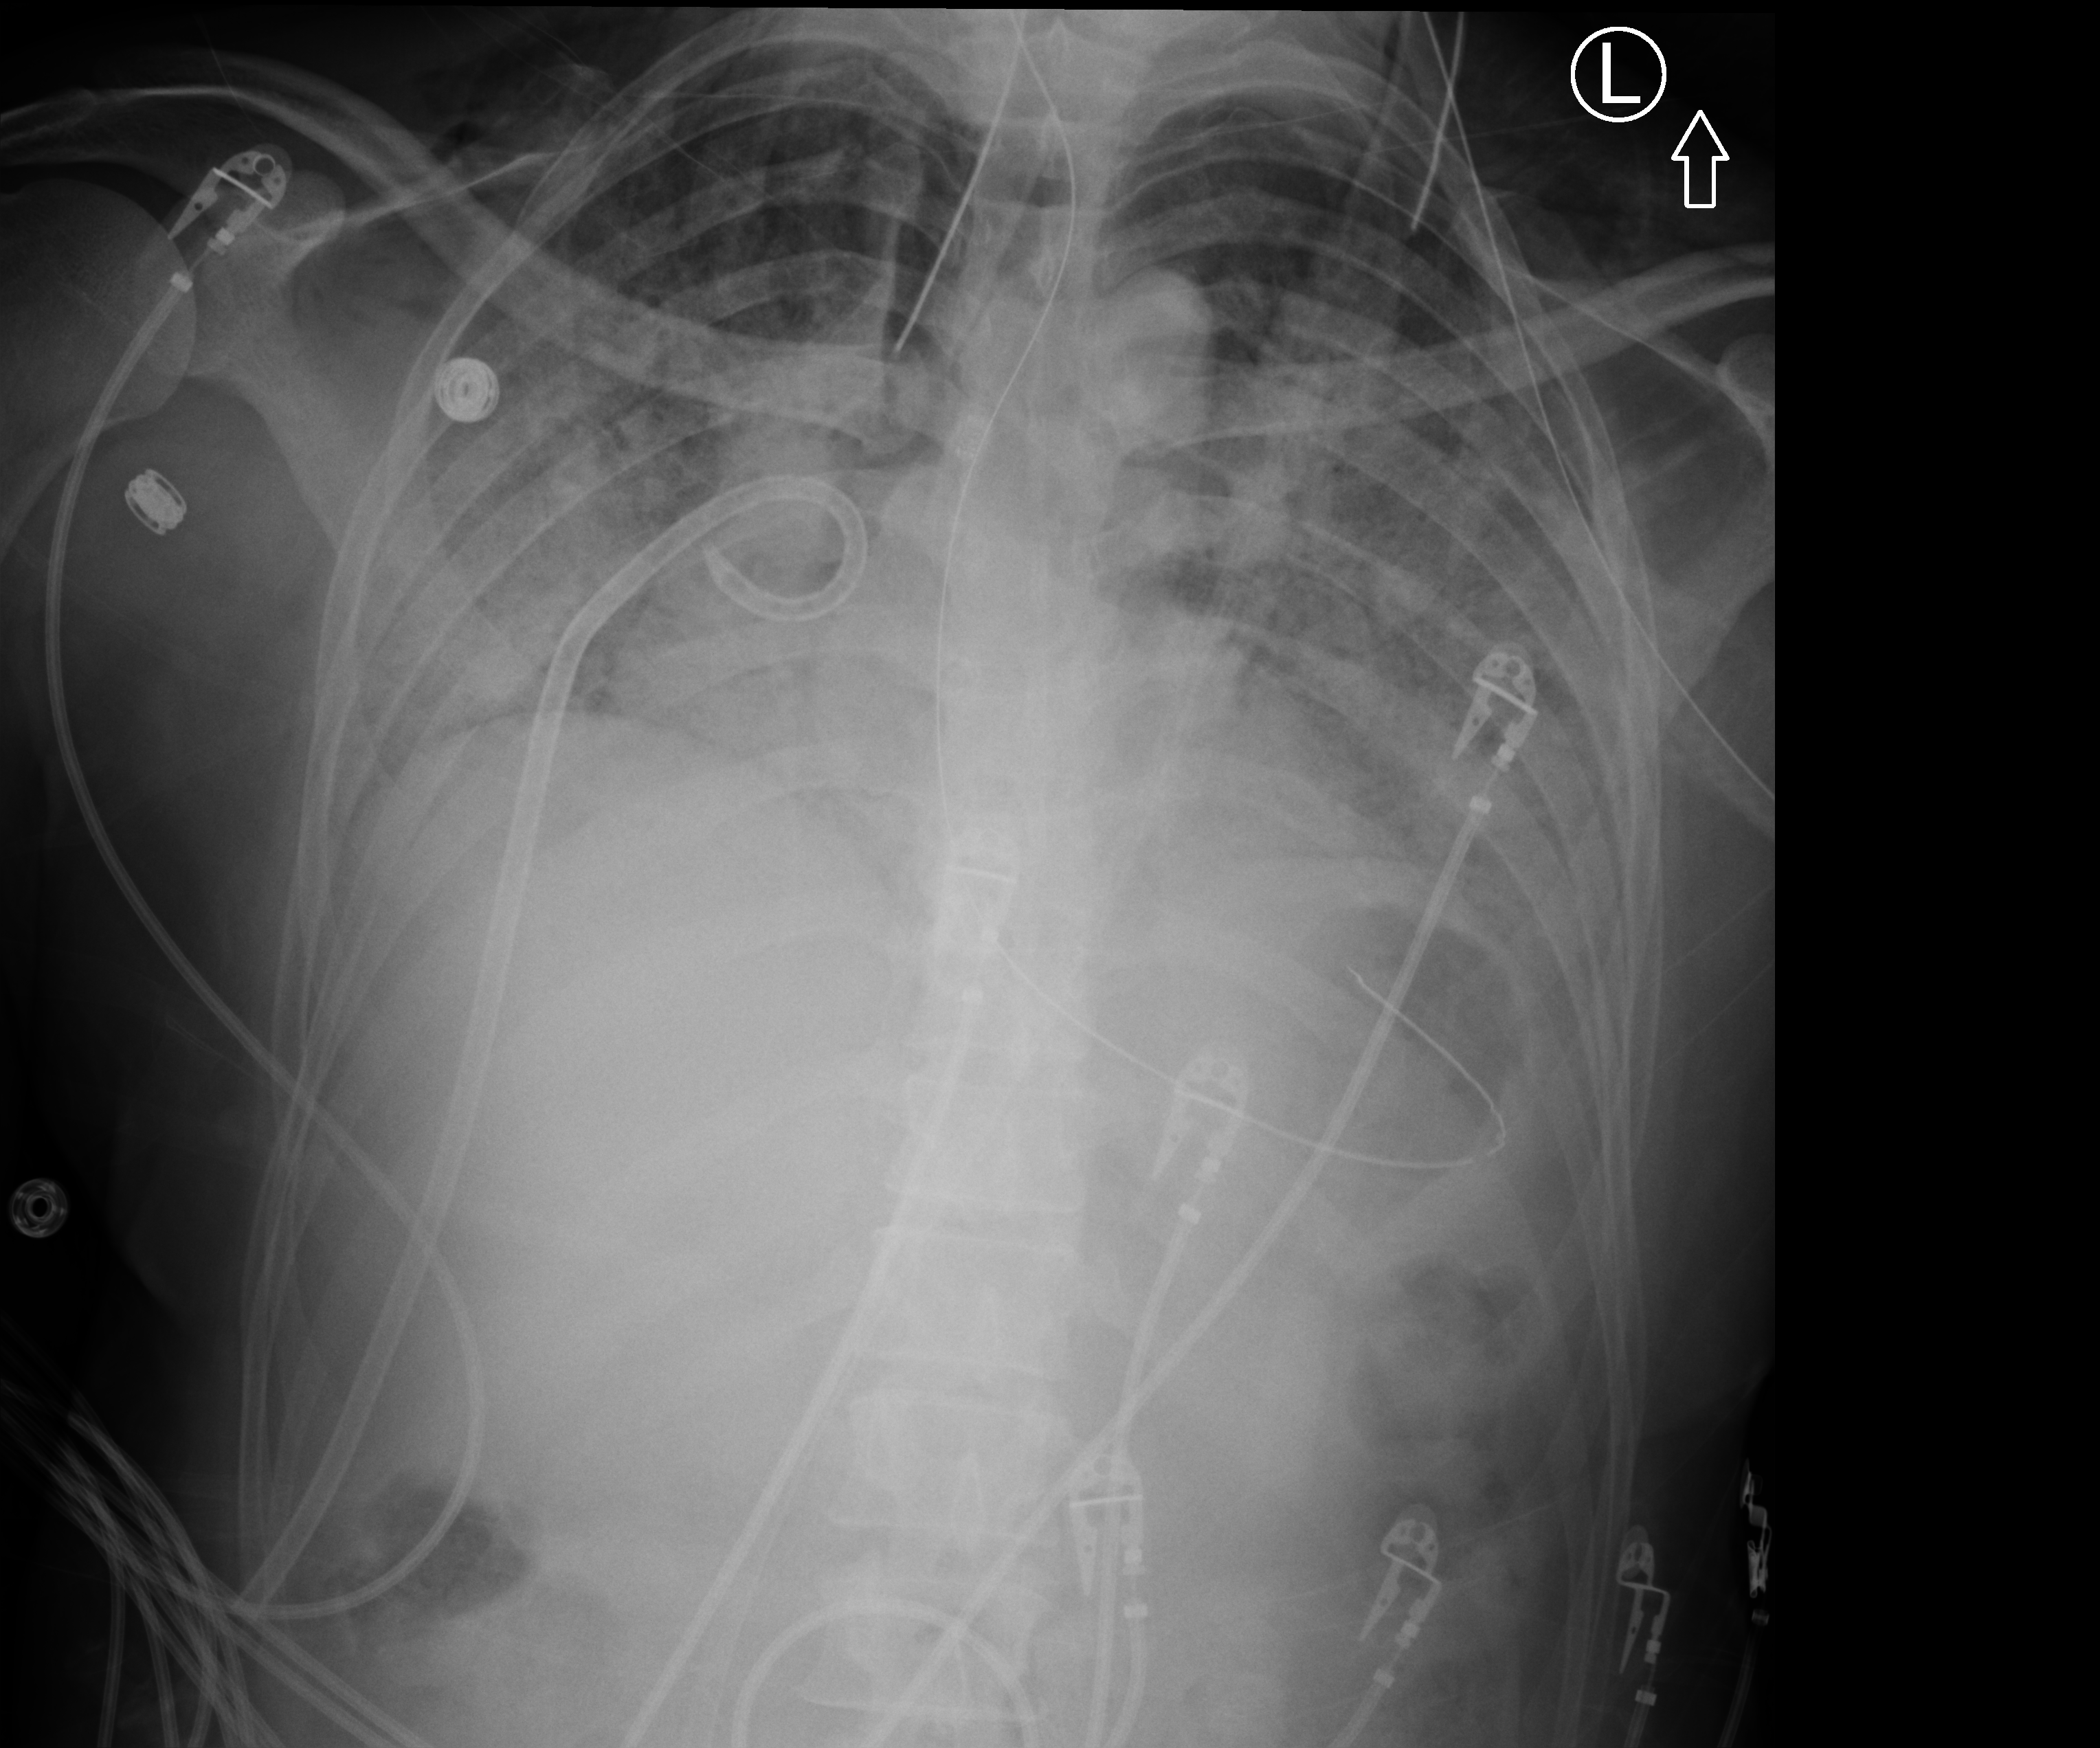
Chest X-ray (portable); anteroposterior (AP) projection. Patient hospitalised with COVID-19, aged 18–59 years.
Admission-level facts for this patient (not findings on this image; timing relative to this image not recorded):
- admitted to intensive care during this hospital stay: yes
- mechanically ventilated during this hospital stay: yes
- smoking status (admission record): never